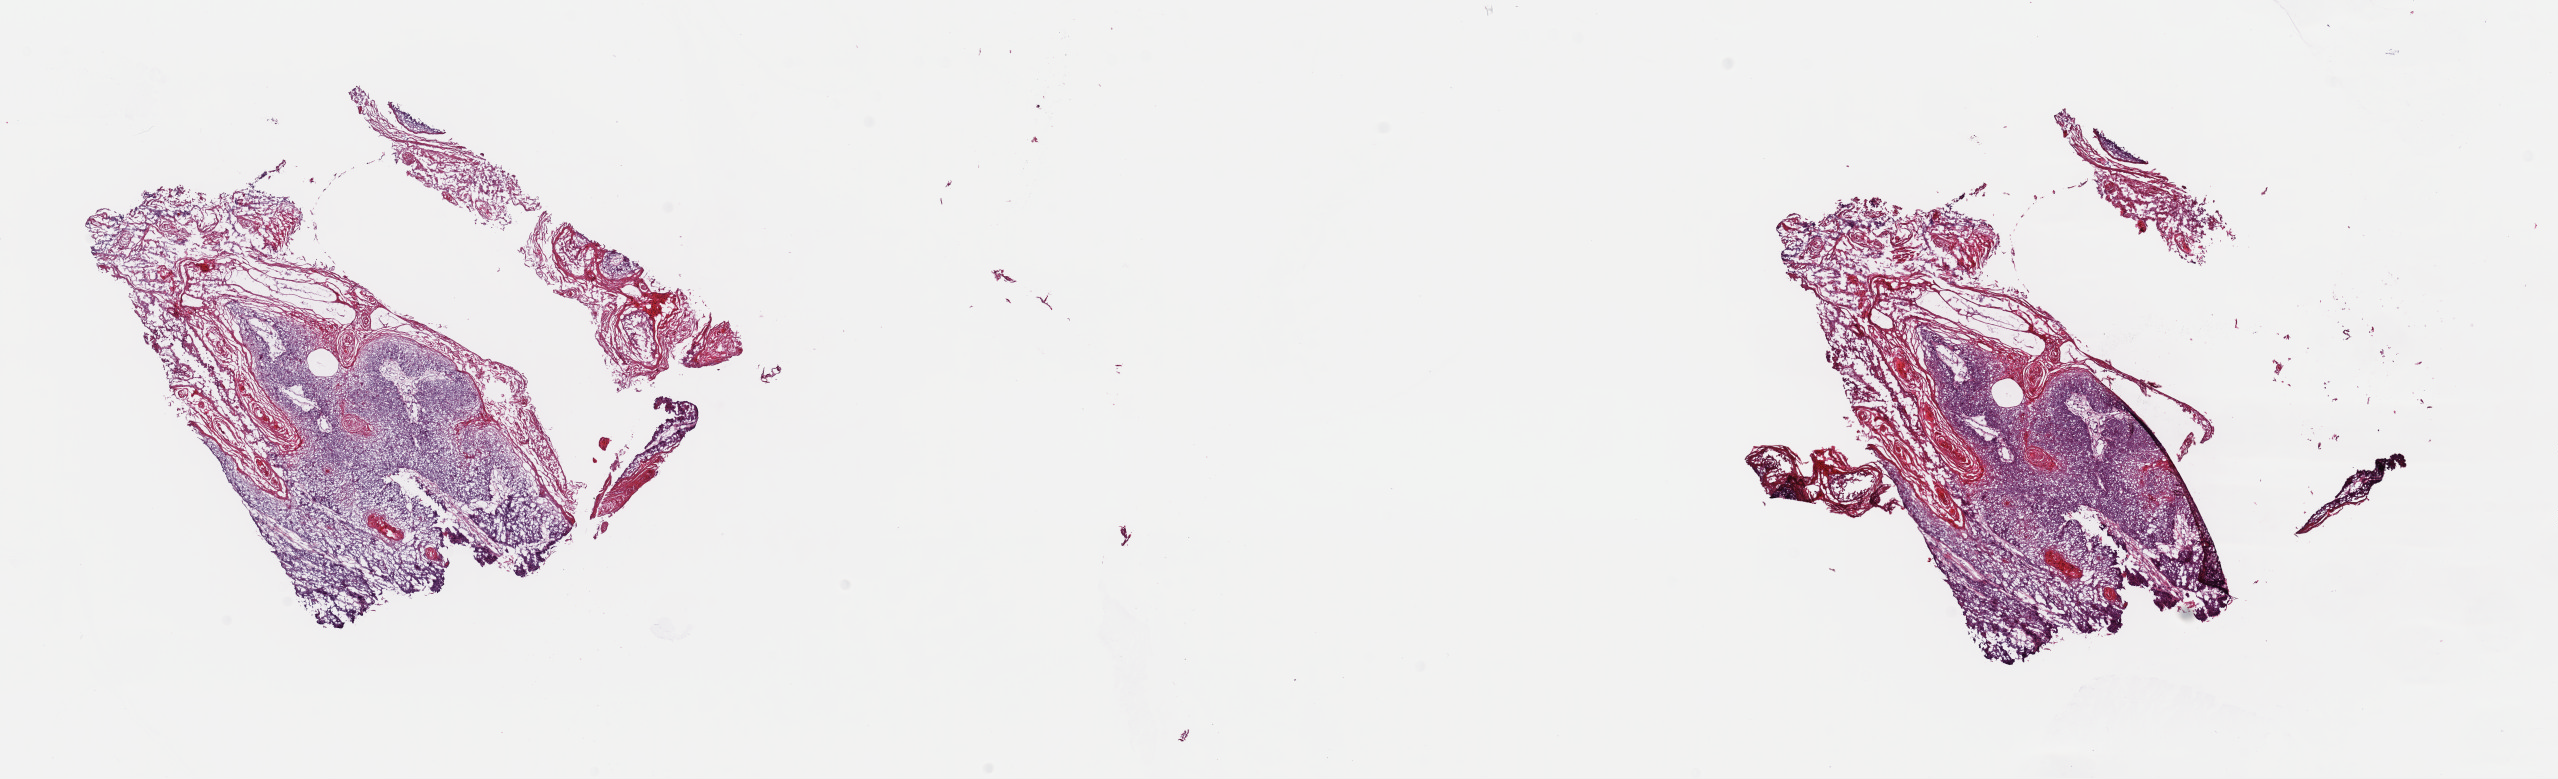
Whole-slide histology image, Hematoxylin and eosin (H&E) stained, whole scanned area (about 20.2 x 6.2 mm) shown as a low-resolution overview; frozen section; primary tumour sample from the bladder. Female, age 43 years at initial diagnosis.
Pathologic diagnosis: Transitional cell carcinoma (anterior wall of bladder).